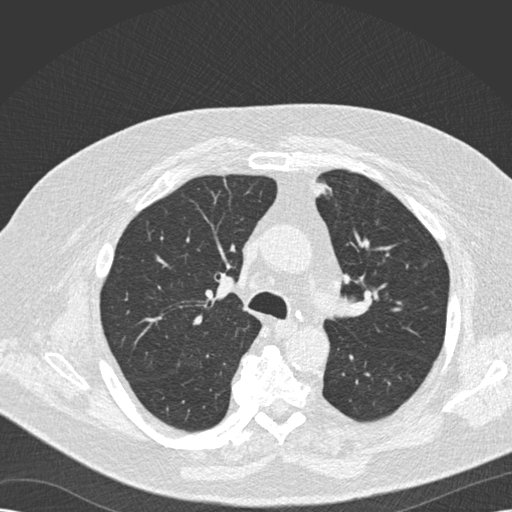
Low-dose screening chest CT, one axial slice. Position 113 of 173 along the scan axis. Reconstruction kernel B30f. 120 kVp. Lung window (W 1500 / L -600 HU). 2 mm slice thickness. 512 × 512 image matrix.
Annotated regions visible in this slice (outlined manually by an expert reader):
- lesion 1 (tumor, upper lobe of left lung): bounding box [x1, y1, x2, y2] px = [315, 184, 333, 197]